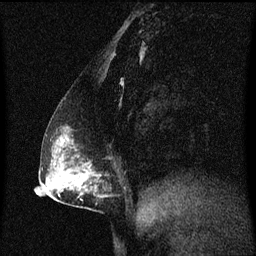
Breast MRI (dynamic contrast-enhanced), one sagittal slice; slice 34 of 60 in the series (ordered by position); dynamic contrast-enhanced series, image 2 of 3 at this slice position (ordered by acquisition); 1.5 T; TE 4.2 ms, TR 8.4 ms; 256 × 256 image matrix, field of view 200 × 200 mm. Patient: female, 40 years. From the clinical record (not read from this slice): setting: breast cancer imaged before/during neoadjuvant chemotherapy; receptor status: triple-negative.
Outlined on this slice (semi-automatically segmented with operator editing):
- analysis volume of interest (the breast-tissue region the enhancement analysis was run in; not a lesion): bounding box (x1, y1, x2, y2) in pixels: (58, 126, 111, 211)
- tumour enhancement mask (voxels above the 70 % enhancement threshold inside the analysis volume of interest): (64, 138, 69, 141)